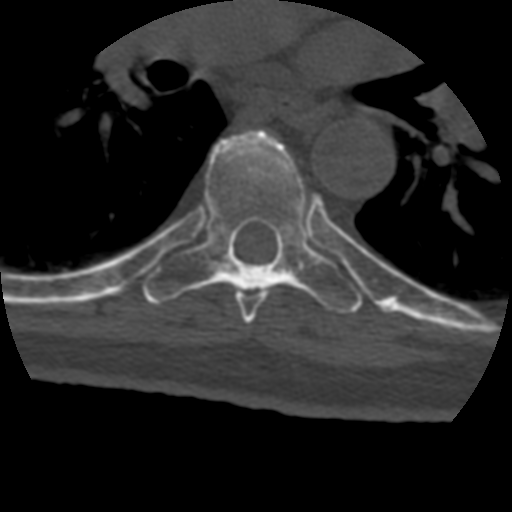
CT including the spine, one axial slice; position 288 of 399 along the scan axis; reconstruction kernel STANDARD; 120 kVp; bone window (W 1800 / L 400 HU); 1.25 mm slice thickness; 512 × 512 image matrix, field of view 160 × 160 mm. Patient age 69 years. From the clinical record (not read from this slice): primary cancer: prostate.
Annotated regions visible in this slice (semi-automatic segmentation, software-assisted and operator-edited):
- T6 vertebra: bounding box <227,283,266,324> (left, top, right, bottom; pixels)
- T7 vertebra: <143,129,363,313>